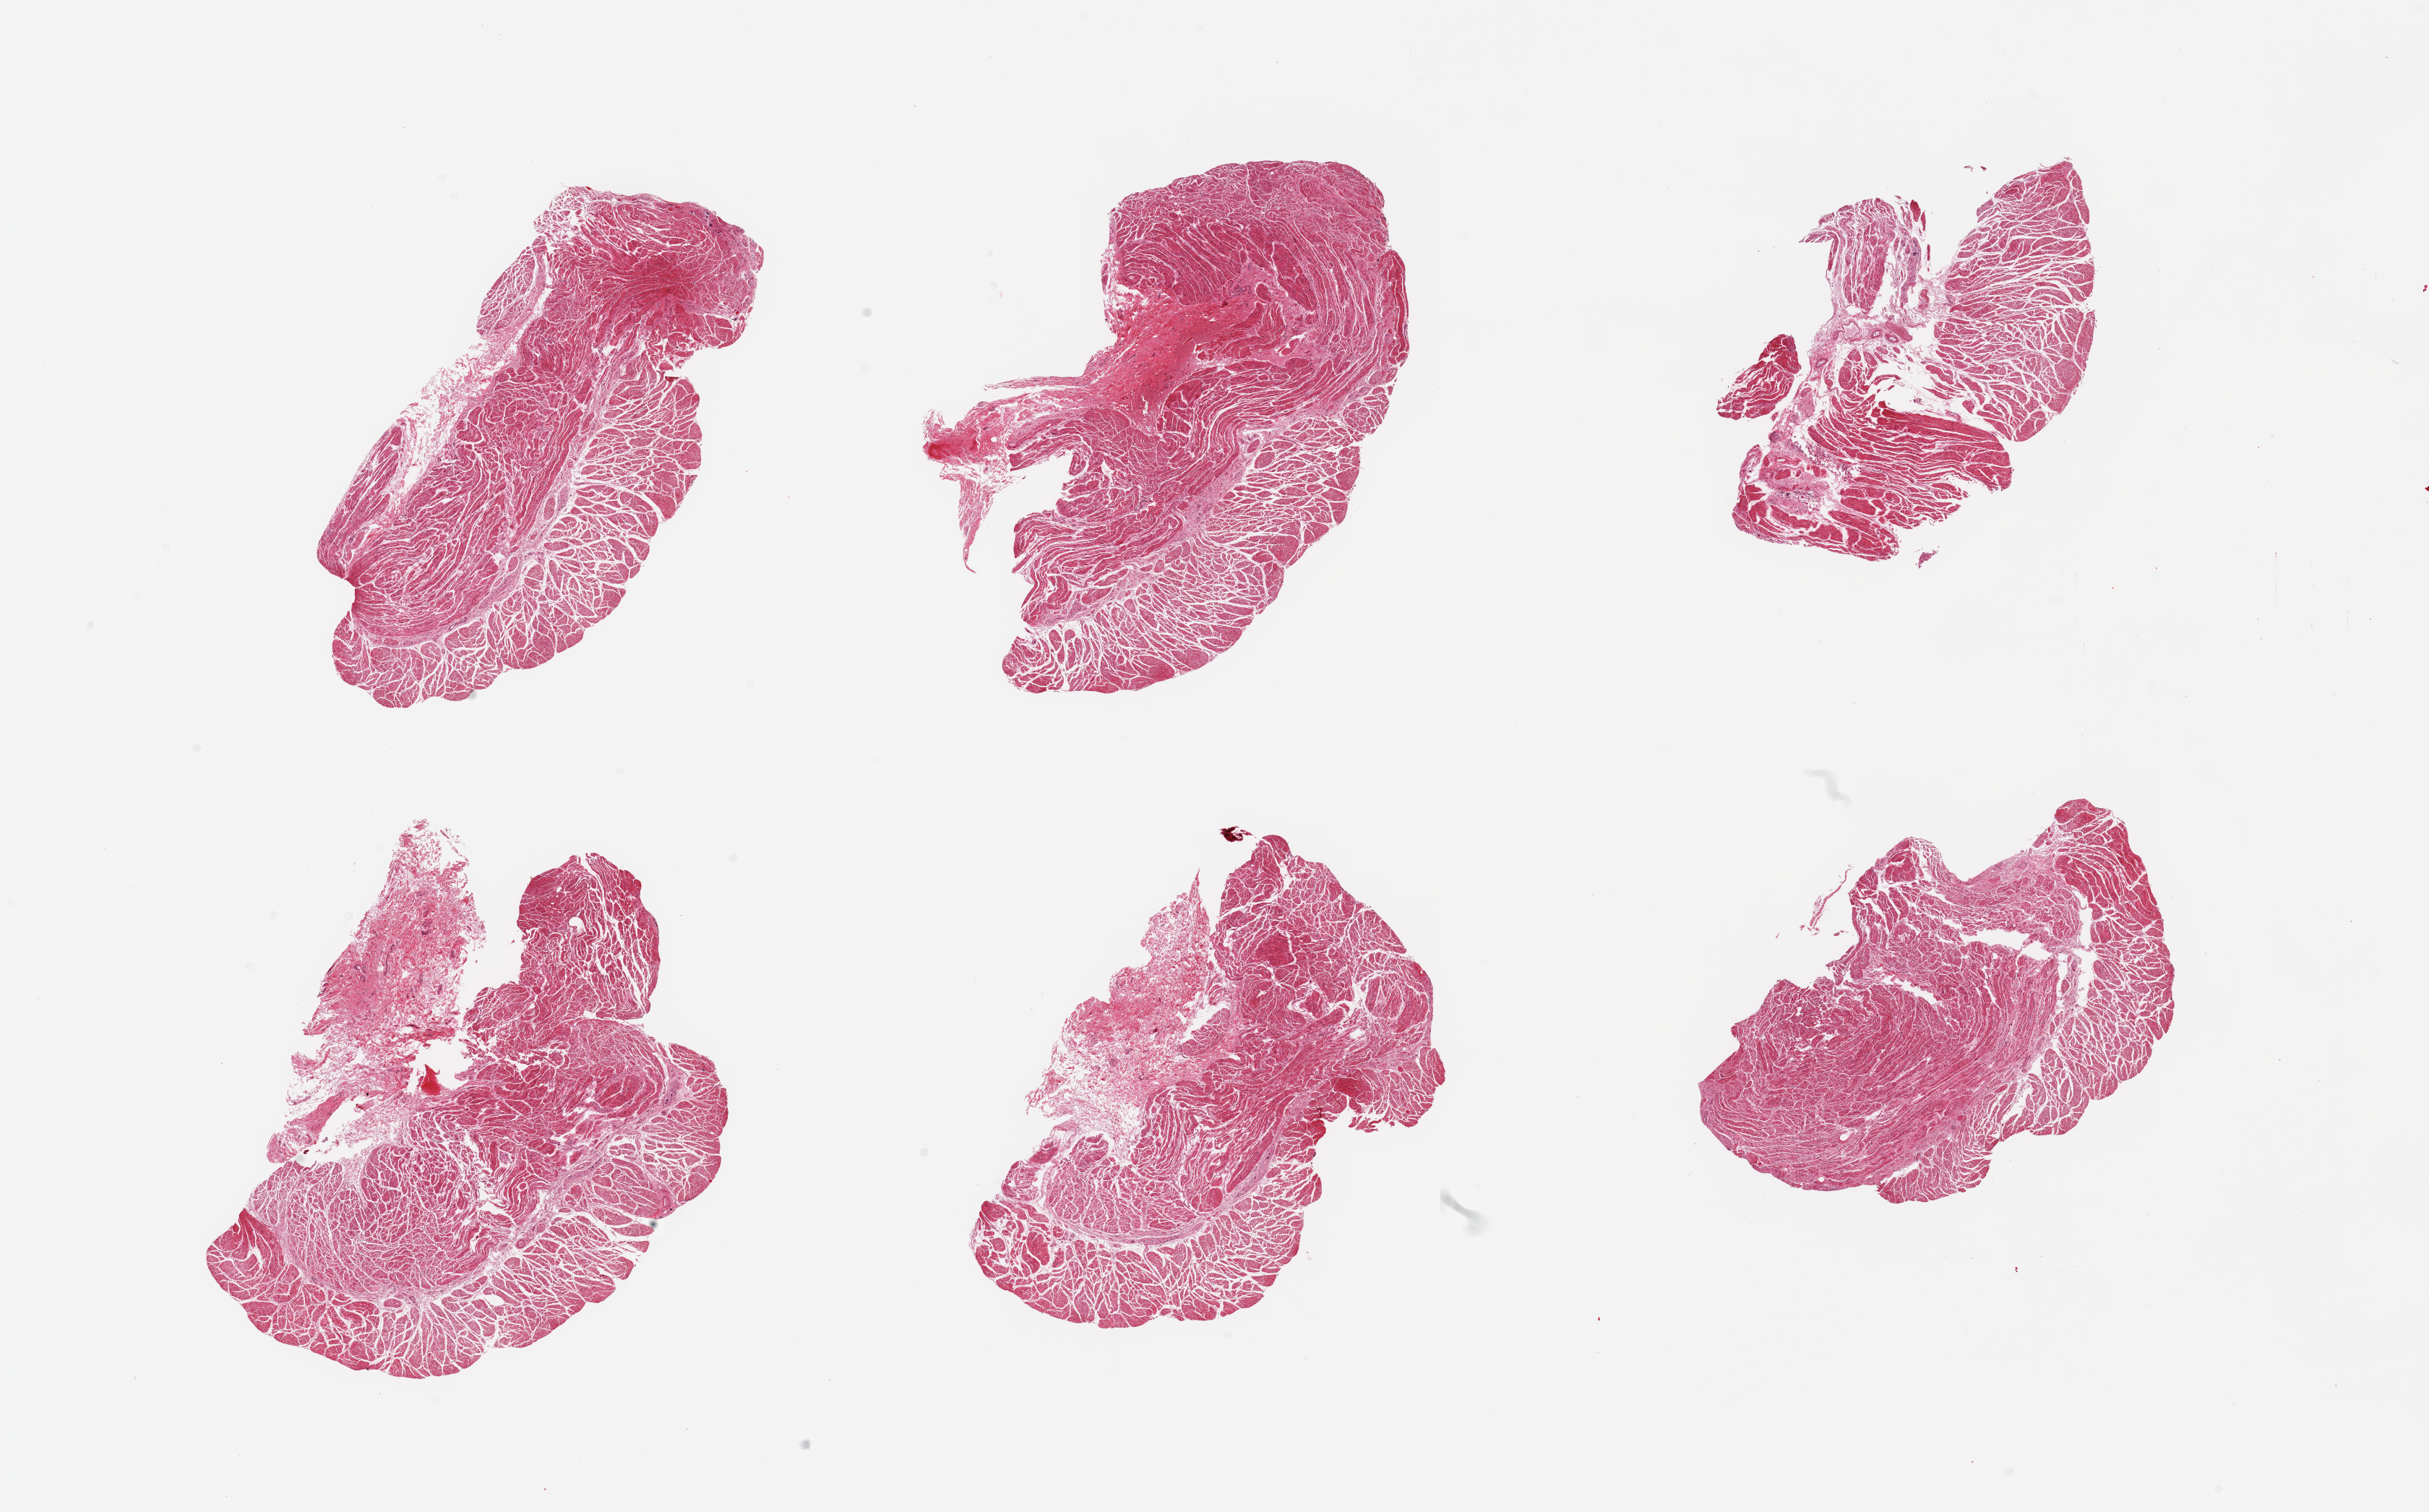
Haematoxylin and eosin whole-slide image, a low-resolution overview of the entire scanned area, about 26.6 x 16.5 mm (from a 20x scan); PAXgene-fixed, paraffin-embedded tissue; sampled site (target tissue): esophageal muscle; donor tissue sample.
- review note (as recorded): 6 pieces confirmed target muscularis